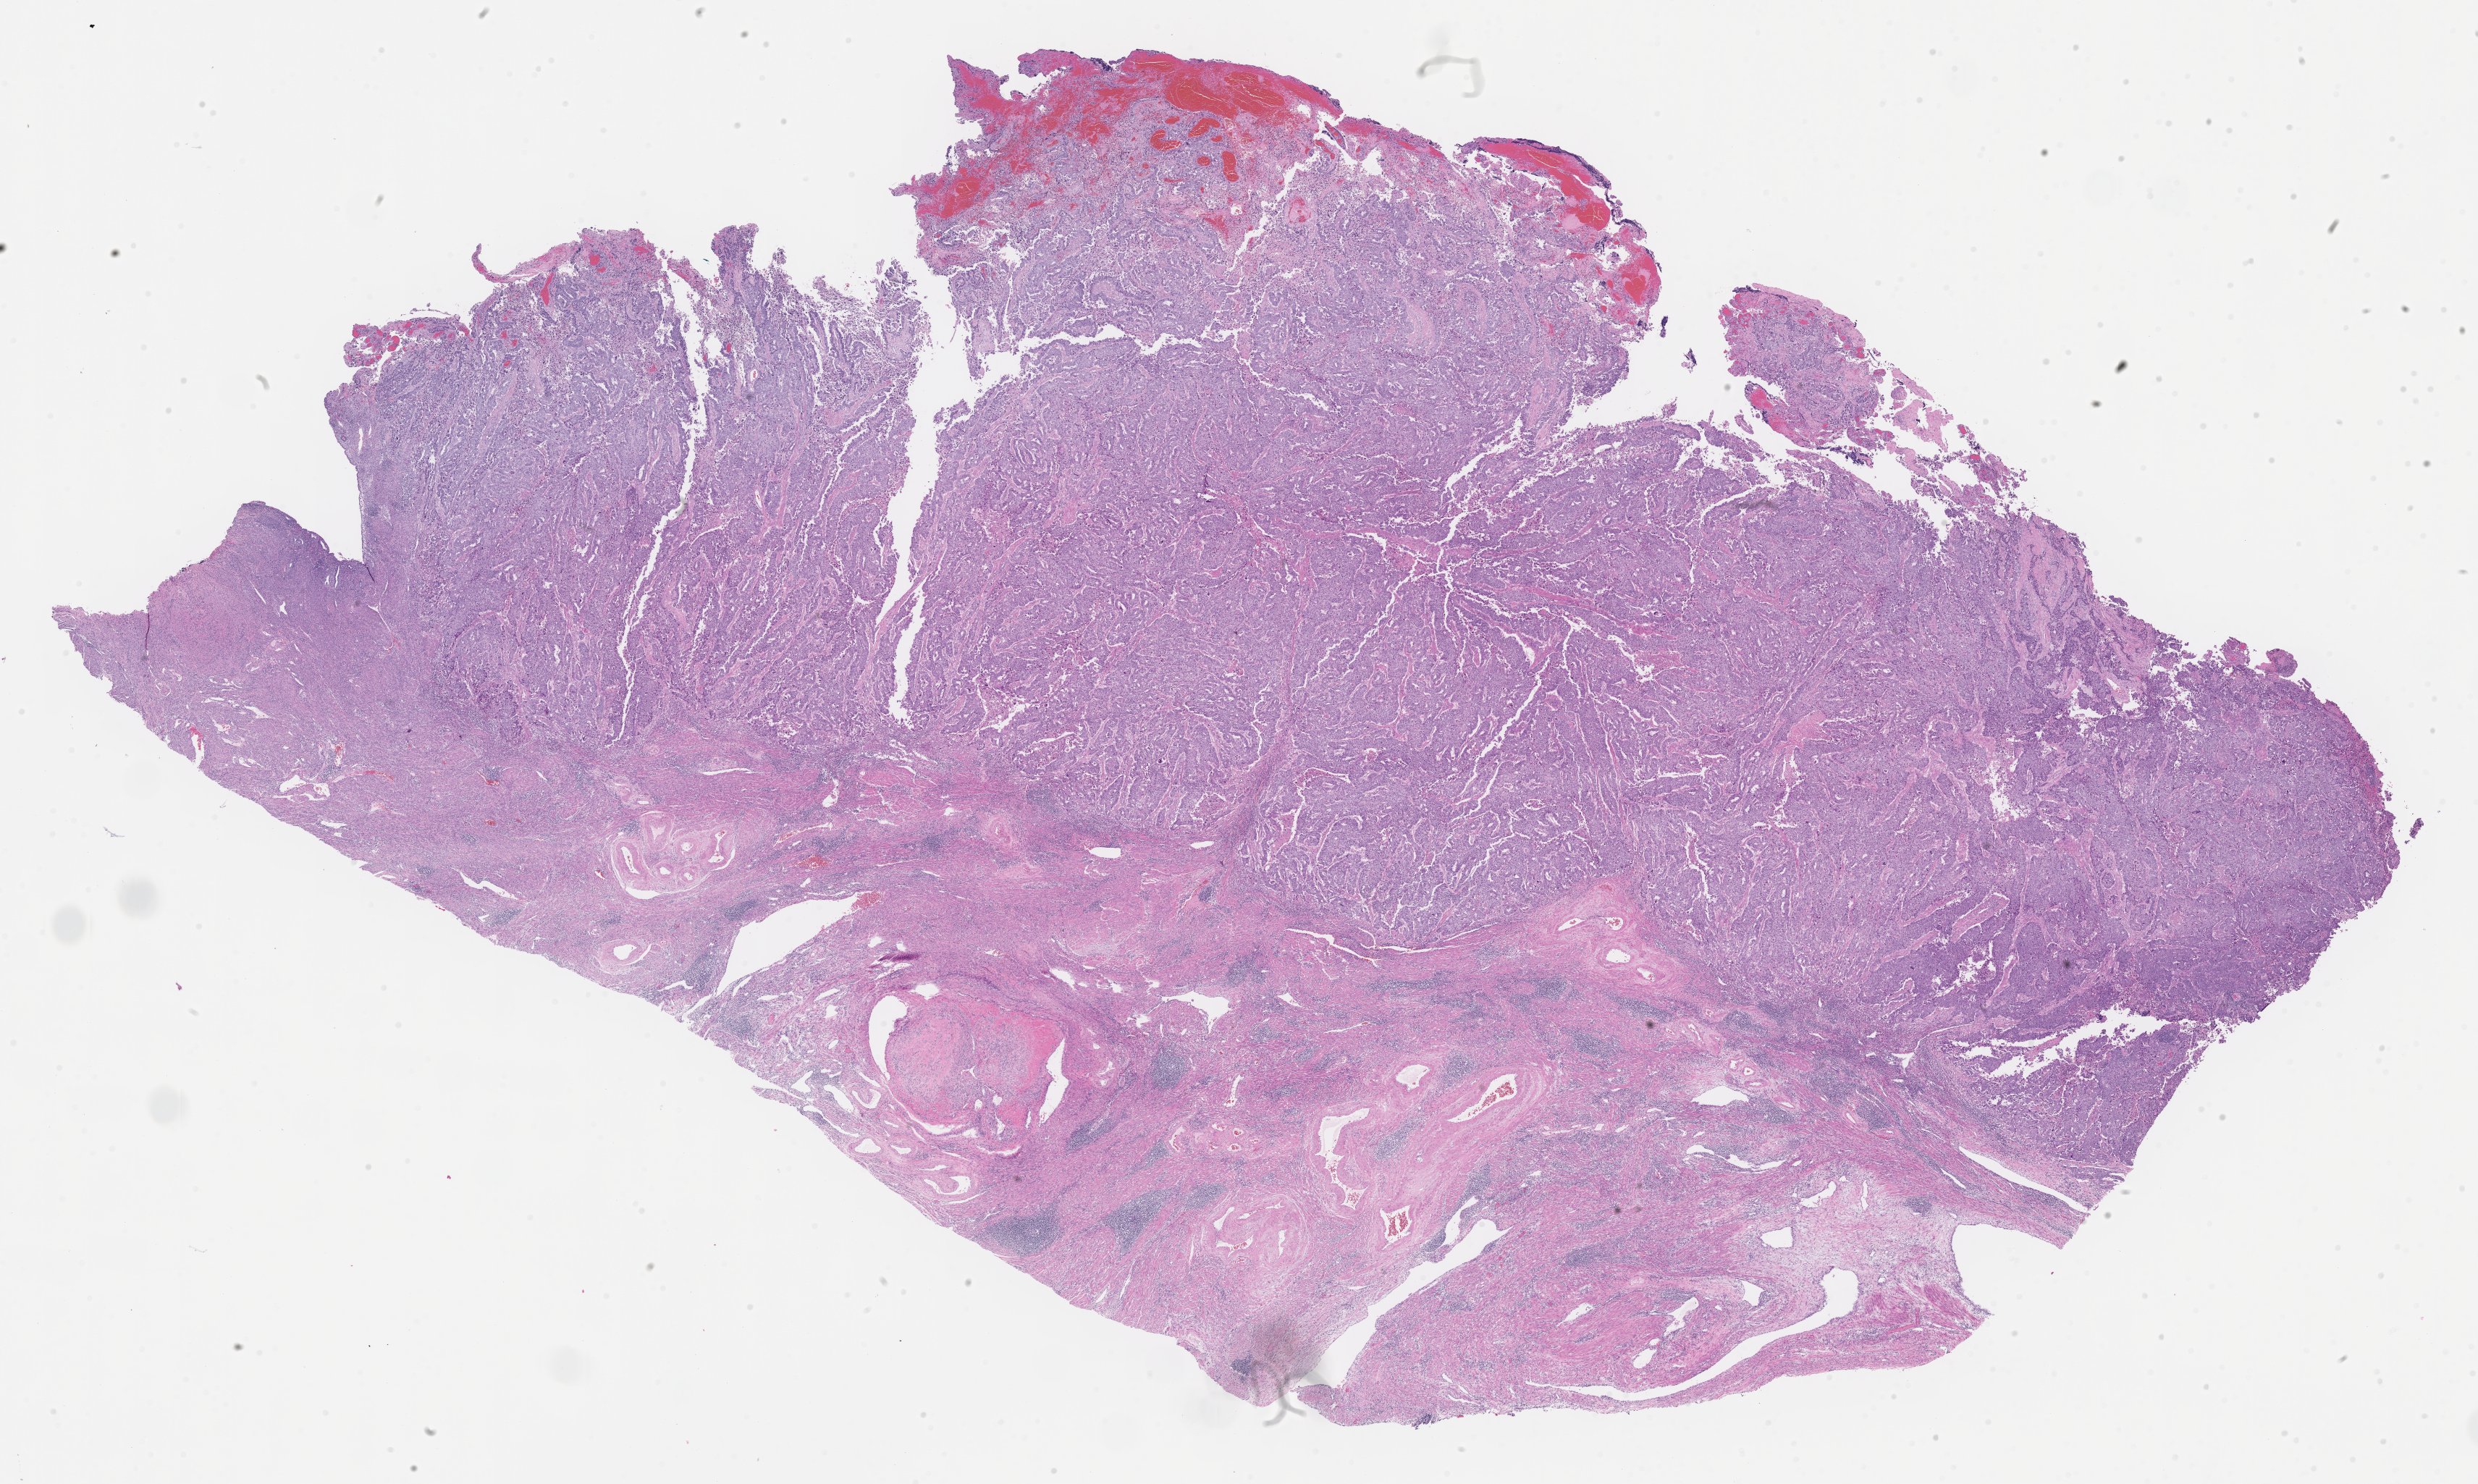
Whole-slide image, H&E stain — whole scanned area (about 27.6 x 16.5 mm) shown as a low-resolution overview, FFPE section, specimen: primary tumor, site: endometrium. Patient: female, age at initial diagnosis 54 years.
Histologic diagnosis: Endometrioid adenocarcinoma, secretory variant.